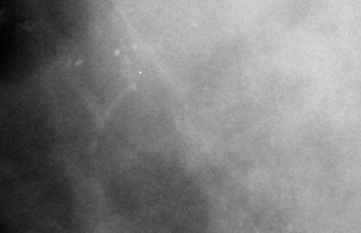
Cropped region of a digitized screen-film mammogram centred on a radiologist-marked abnormality; right breast; MLO view.
Marked abnormality: calcifications, morphology pleomorphic, distribution linear; BI-RADS assessment category 4; pathology result (as recorded, not read from the image): malignant.